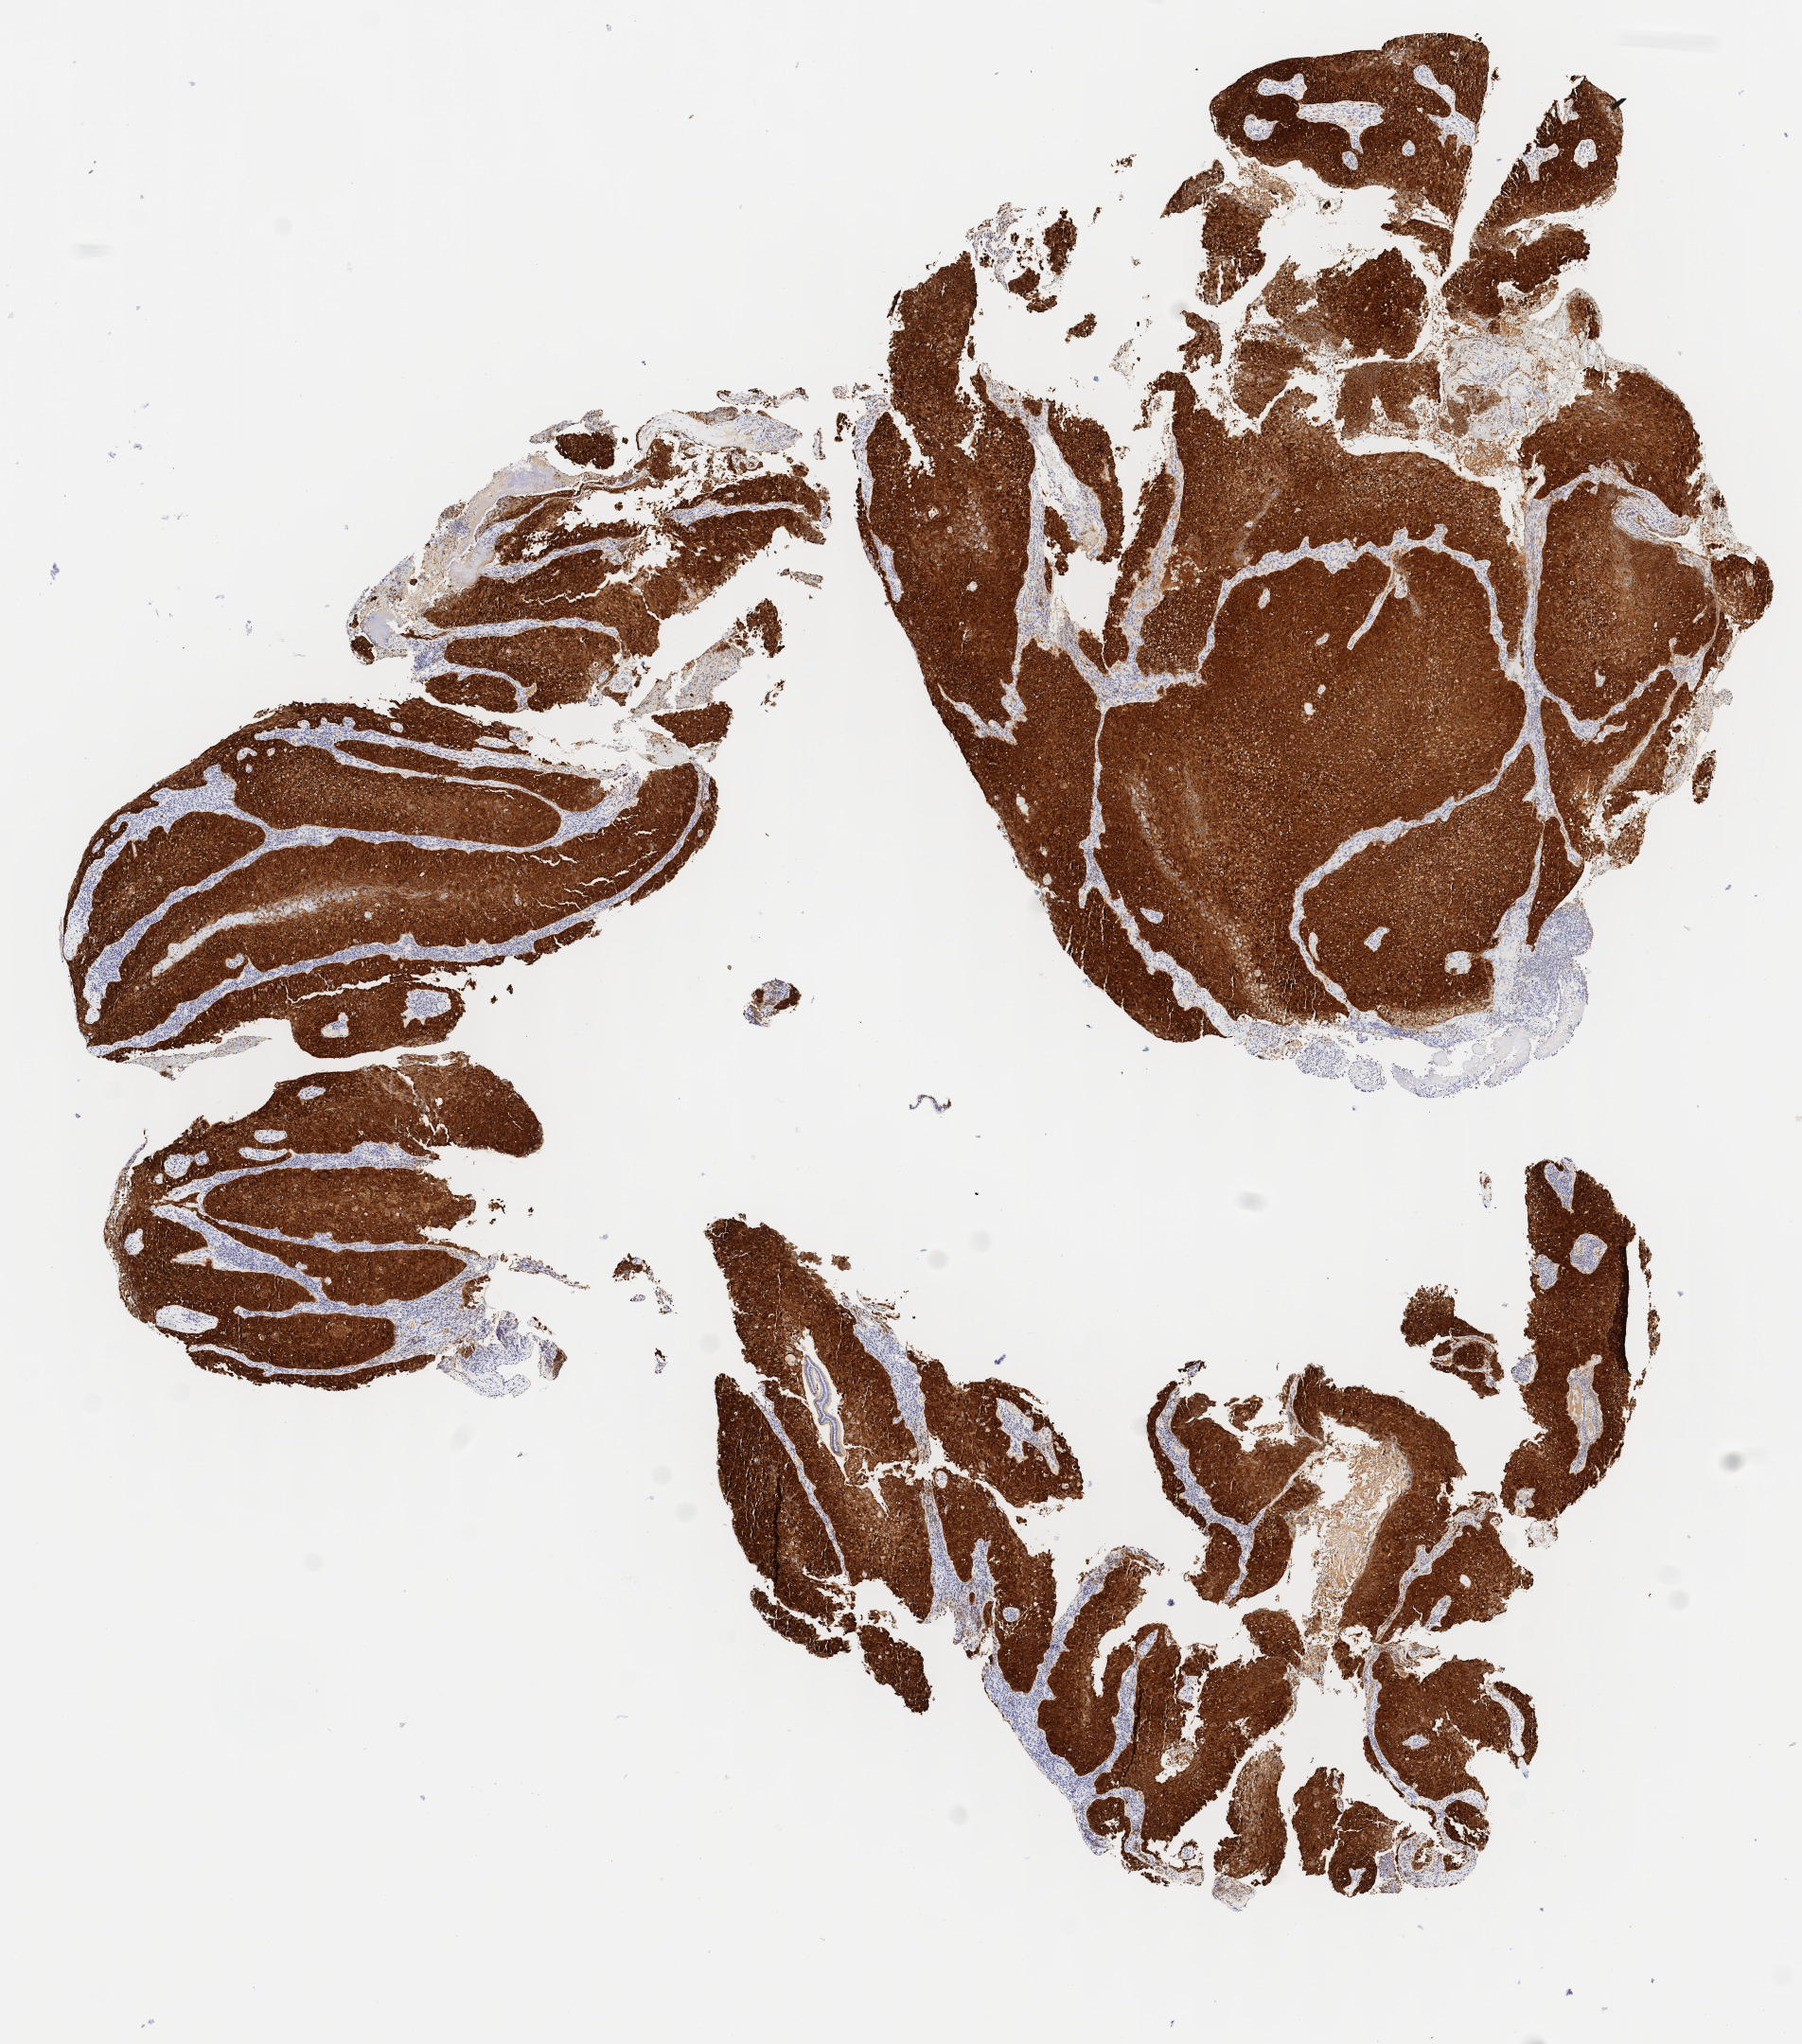
Whole-slide image, immunohistochemical stain for p16 (p16INK4a), whole scanned area (about 7.6 x 8.6 mm) shown as a low-resolution overview; tumor tissue; anatomic site: cervix. Female patient, age 50 years.
Diagnosis: Squamous cell carcinoma, large cell, nonkeratinizing, NOS.